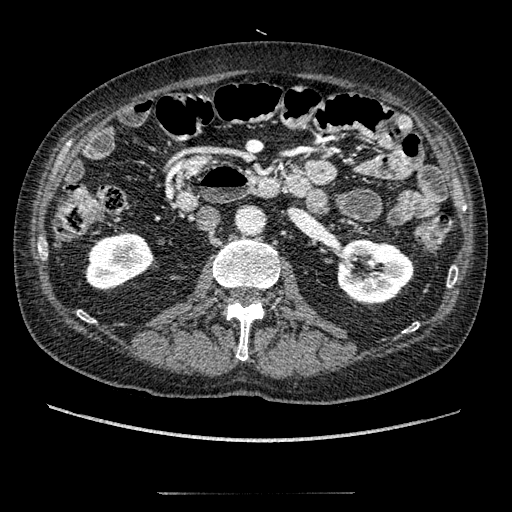
Contrast-enhanced abdominal CT, one axial slice. Slice 78 of 274 in the series (ordered by position). 120 kVp. Intravenous contrast given. Soft-tissue window (W 400 / L 40 HU). 1.25 mm slice thickness. 512 × 512 image matrix, field of view 381 × 381 mm. Patient: male, 69 years. From the clinical record (not read from this slice): diagnosis: adrenocortical carcinoma; tumour side: left adrenal; tumour size at pathology: 6.1 cm.
Annotated regions visible in this slice (semi-automatic segmentation, software-assisted and operator-edited):
- mass: box from (x=307, y=190) to (x=327, y=212) px